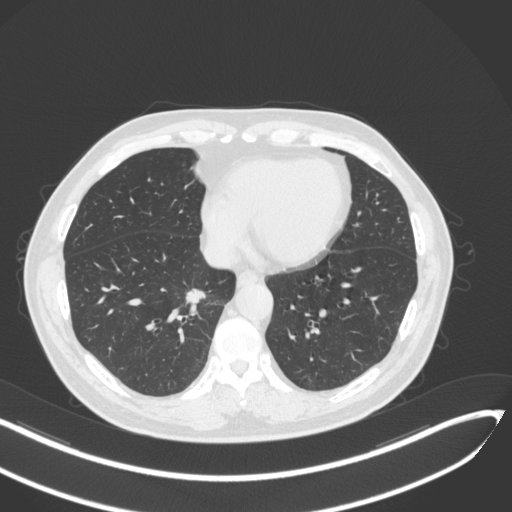
Chest CT, one axial slice. Slice 126 of 429 in the series (ordered by position). Reconstruction kernel B31f. Lung window (W 1500 / L -600 HU). 1 mm slice thickness. 512 × 512 image matrix. Patient: male, 62 years. Case-level facts recorded for this patient, not image findings: clinical TNM (as recorded): T1b N0 M0; histopathological grade: G2.
Structures marked on this image (bounding box drawn by a radiologist):
- lung tumour (recorded histology: adenocarcinoma): bounding box (x1, y1, x2, y2) in pixels: (184, 286, 208, 308)